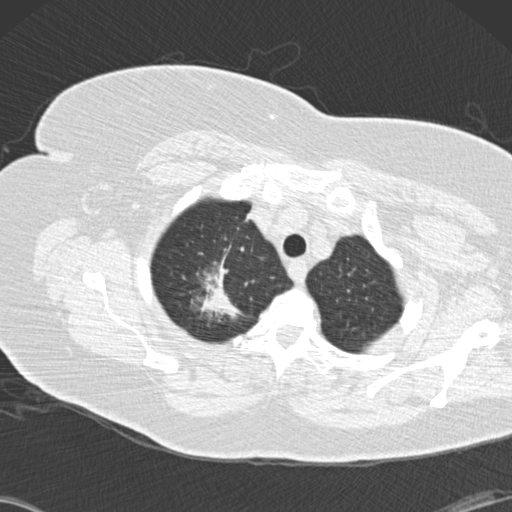
Low-dose screening chest CT, one axial slice. Lung window (W 1500 / L -600 HU). 2 mm slice thickness. 512 × 512 image matrix, field of view 350 × 350 mm.
Outlined on this slice (expert manual segmentation):
- lesion 1 (tumor, upper lobe of right lung): bounding box (x1, y1, x2, y2) in pixels: (198, 264, 242, 317)